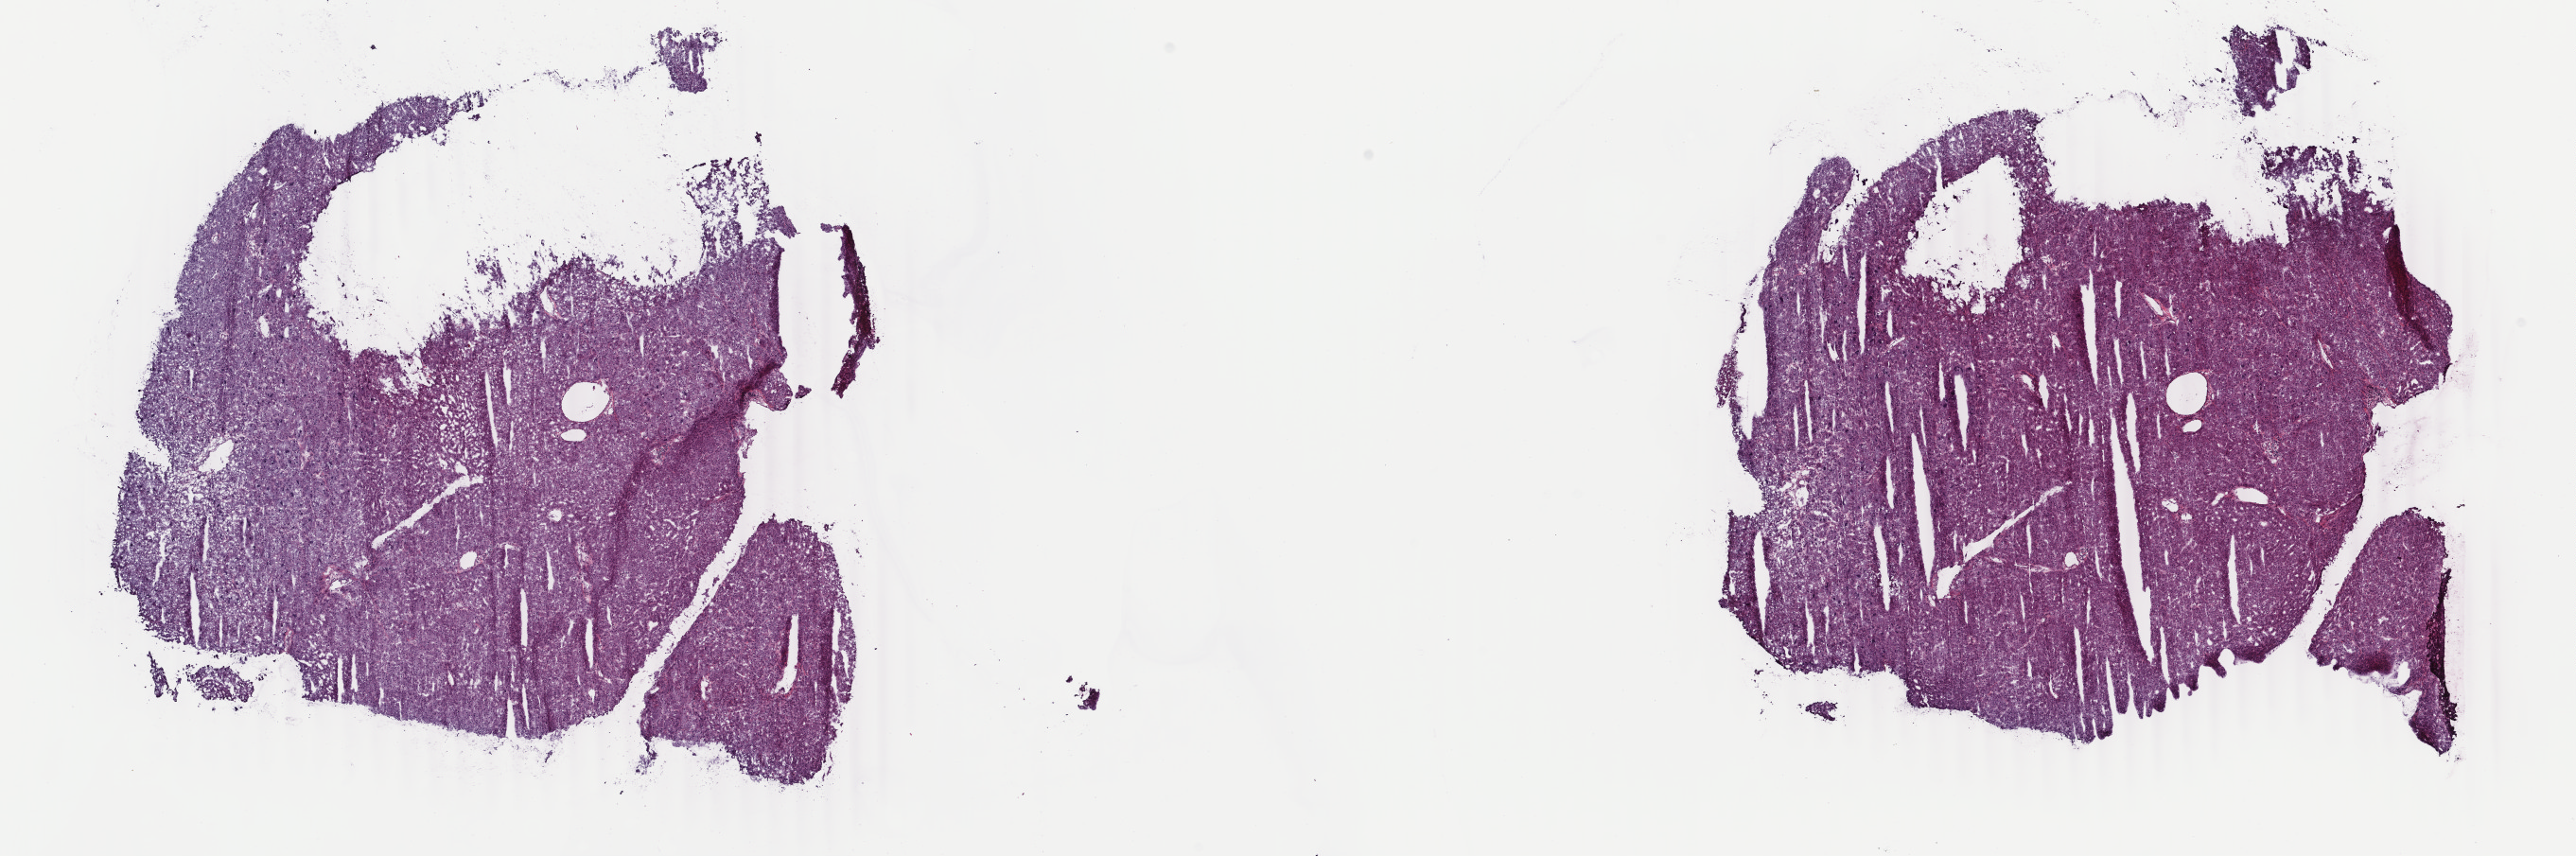
H&E whole-slide image, whole scanned area (about 21.7 x 7.2 mm) shown as a low-resolution overview. Frozen section from the top of the tissue portion. Sample: primary tumour, adrenal cortex. Patient: female, age at initial diagnosis 52 years. Slide review estimates, as recorded: tumour cells 90%, tumour nuclei 90%, normal cells 0%, stromal cells 0%, necrosis 10%. Inflammatory infiltration, as recorded: lymphocyte infiltration 40%, monocyte infiltration 20%, neutrophil infiltration 20%.
* diagnosis: Adrenal cortical carcinoma (cortex of adrenal gland)
* laterality: left